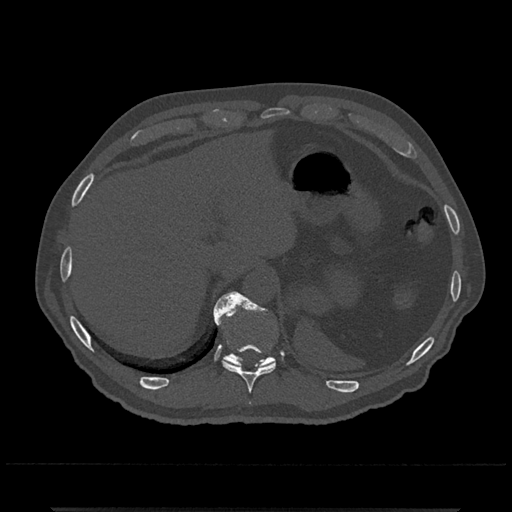
CT including the spine, one axial slice; position 532 of 797 along the scan axis; reconstruction kernel Br40s/3; 120 kVp; bone window (W 1800 / L 400 HU); 0.5 mm slice thickness; 512 × 512 image matrix, field of view 393 × 393 mm. Male patient, age 67 years. From the clinical record (not read from this slice): primary cancer: prostate.
Structures marked on this image (semi-automatically segmented with operator editing):
- T10 vertebra: bounding box (x1, y1, x2, y2) in pixels: (215, 292, 276, 405)
- T11 vertebra: (213, 293, 276, 367)